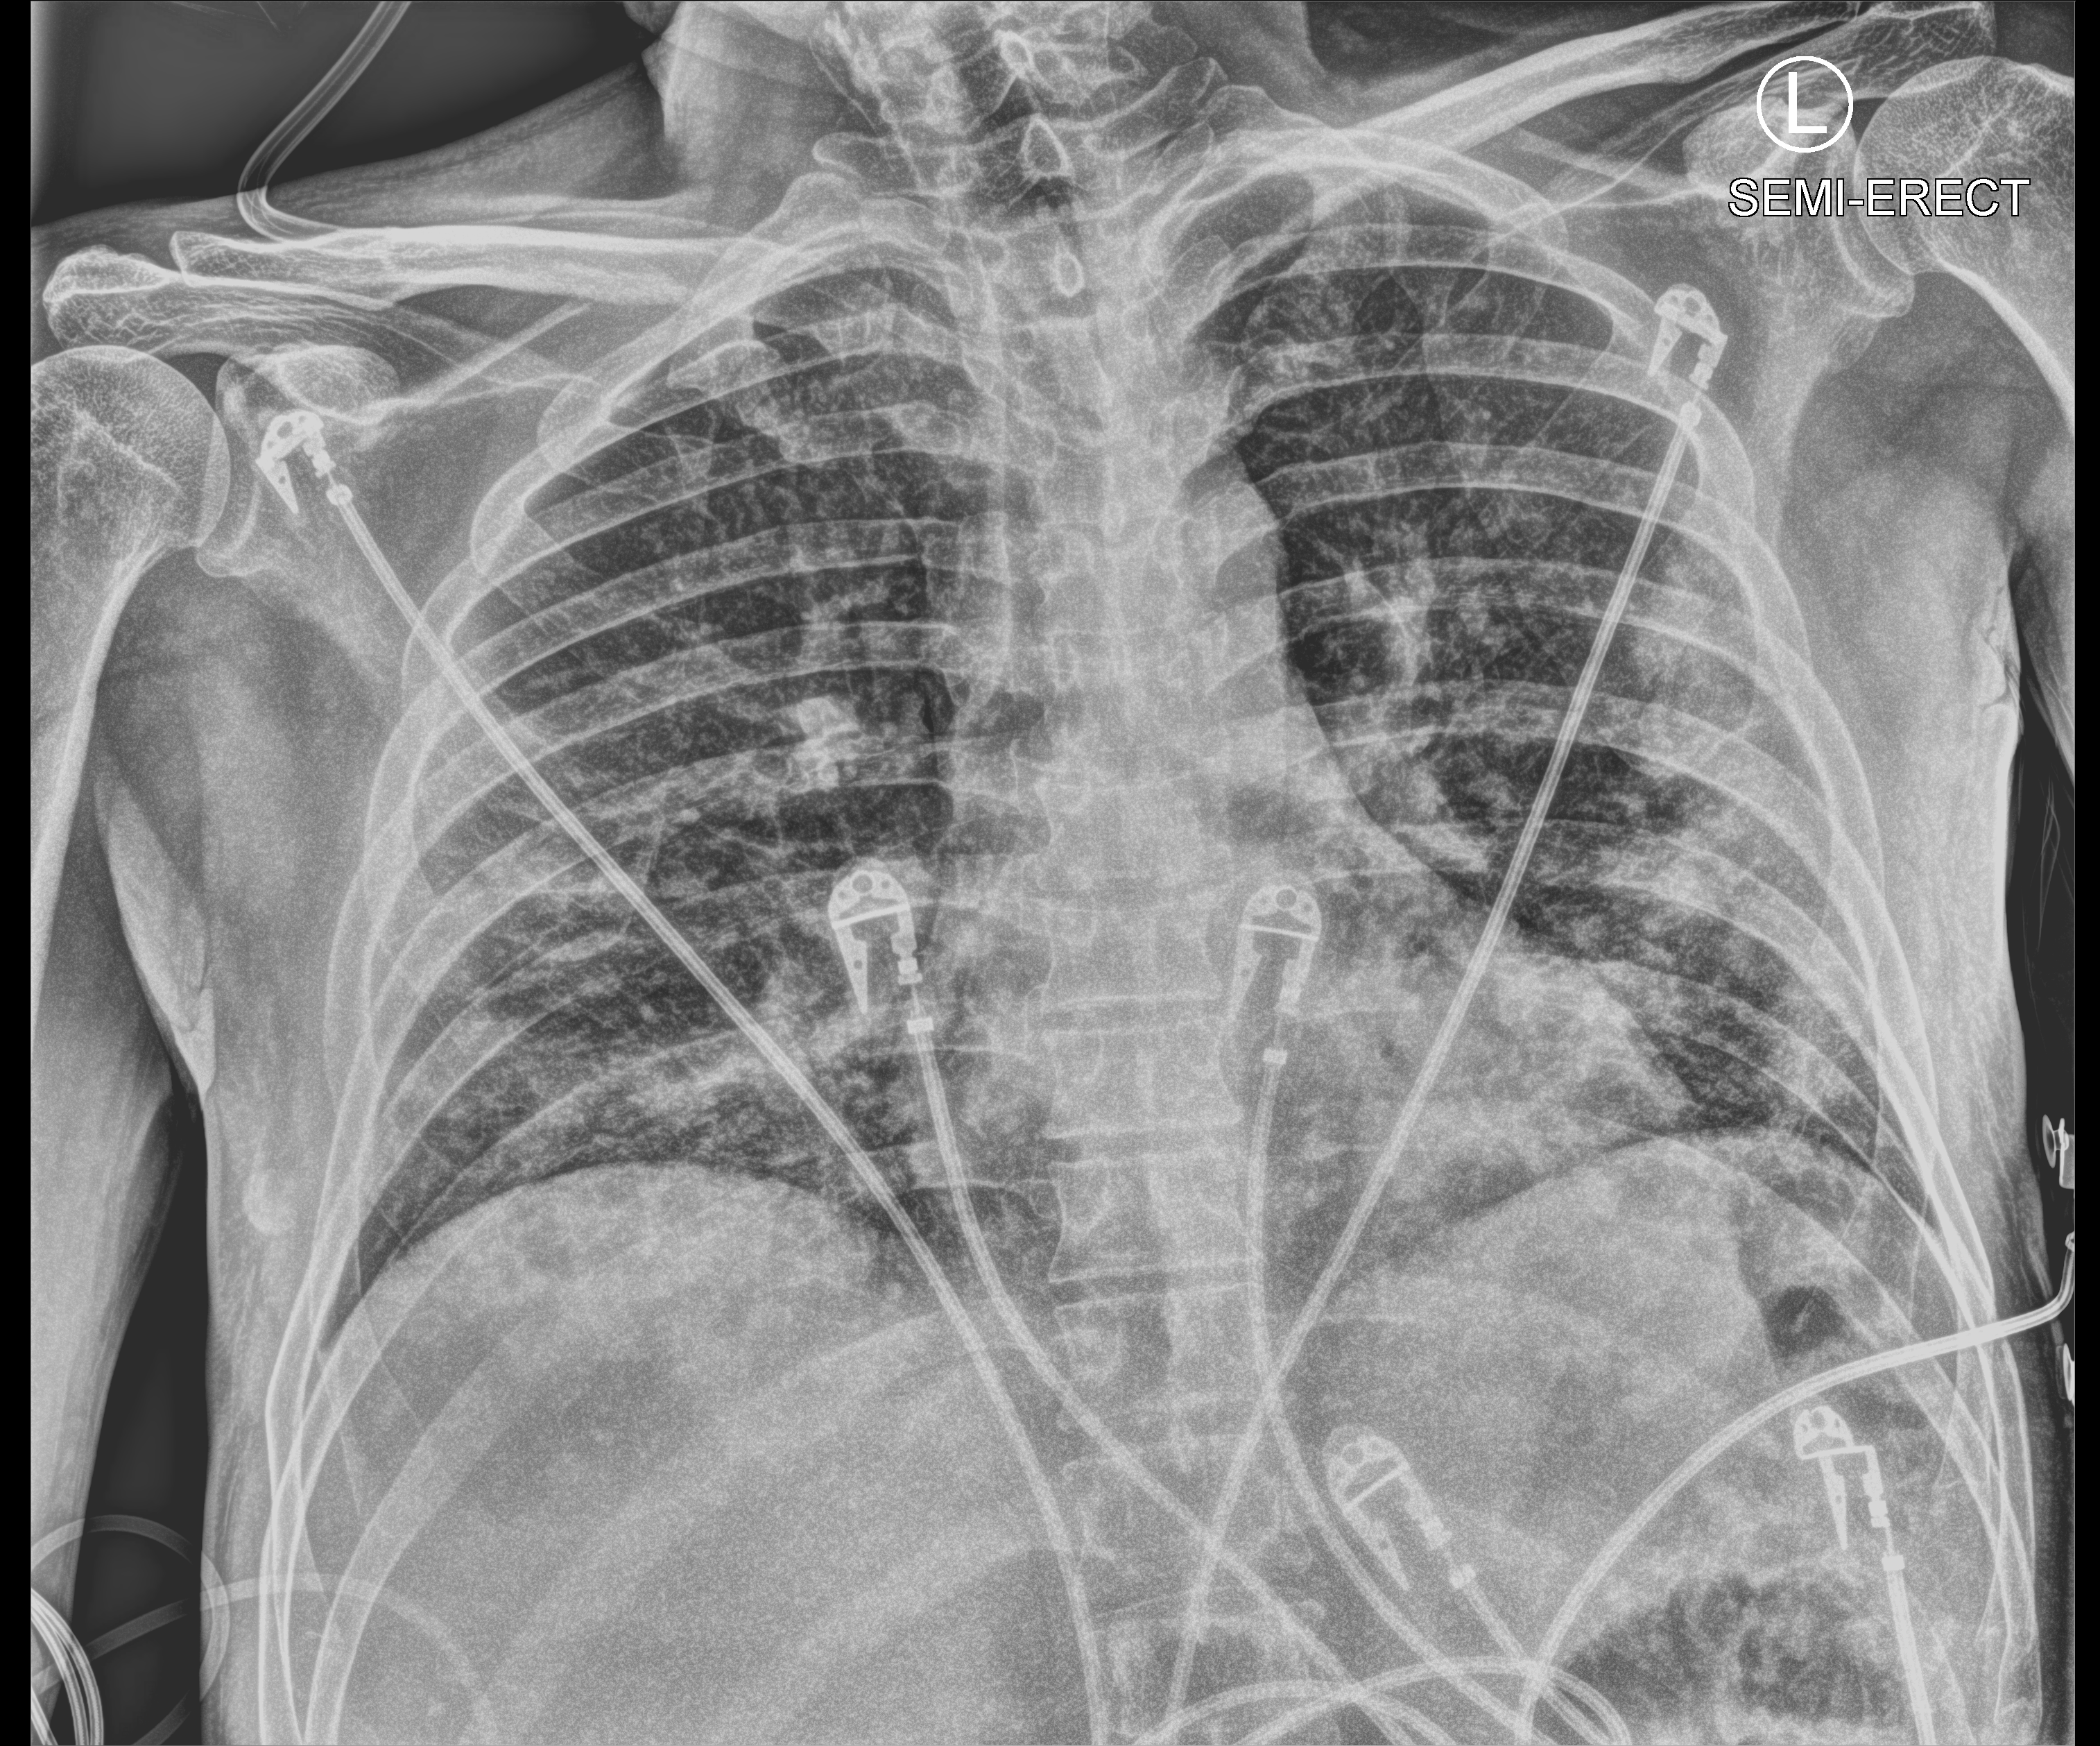
Portable chest radiograph; anteroposterior (AP) projection. Male patient hospitalised with COVID-19, age 18–59 years.
Admission-level facts for this patient (not findings on this image; timing relative to this image not recorded):
- hypertension (admission record): yes